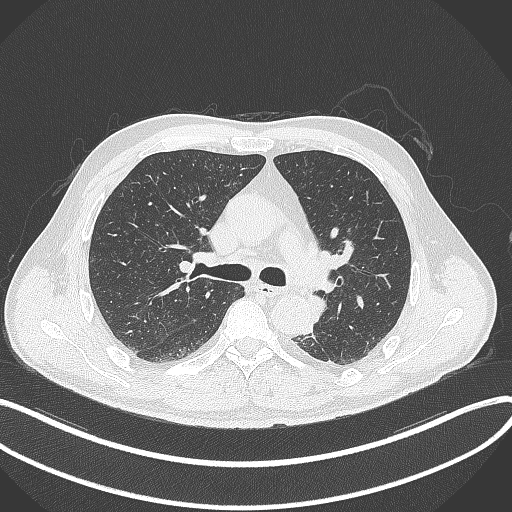
Chest CT, one axial slice. Slice 222 of 329 in the series (ordered by position). Reconstruction kernel B70f. 120 kVp. Lung window (W 1500 / L -600 HU). 1 mm slice thickness. 512 × 512 image matrix, field of view 400 × 400 mm. Male patient, age 59 years. From the clinical record (not read from this slice): clinical TNM (as recorded): T2a N2 M0.
Outlined on this slice (rectangle marked by the reading radiologist):
- lung tumour (recorded histology: squamous cell carcinoma): box from (x=308, y=292) to (x=330, y=325) px